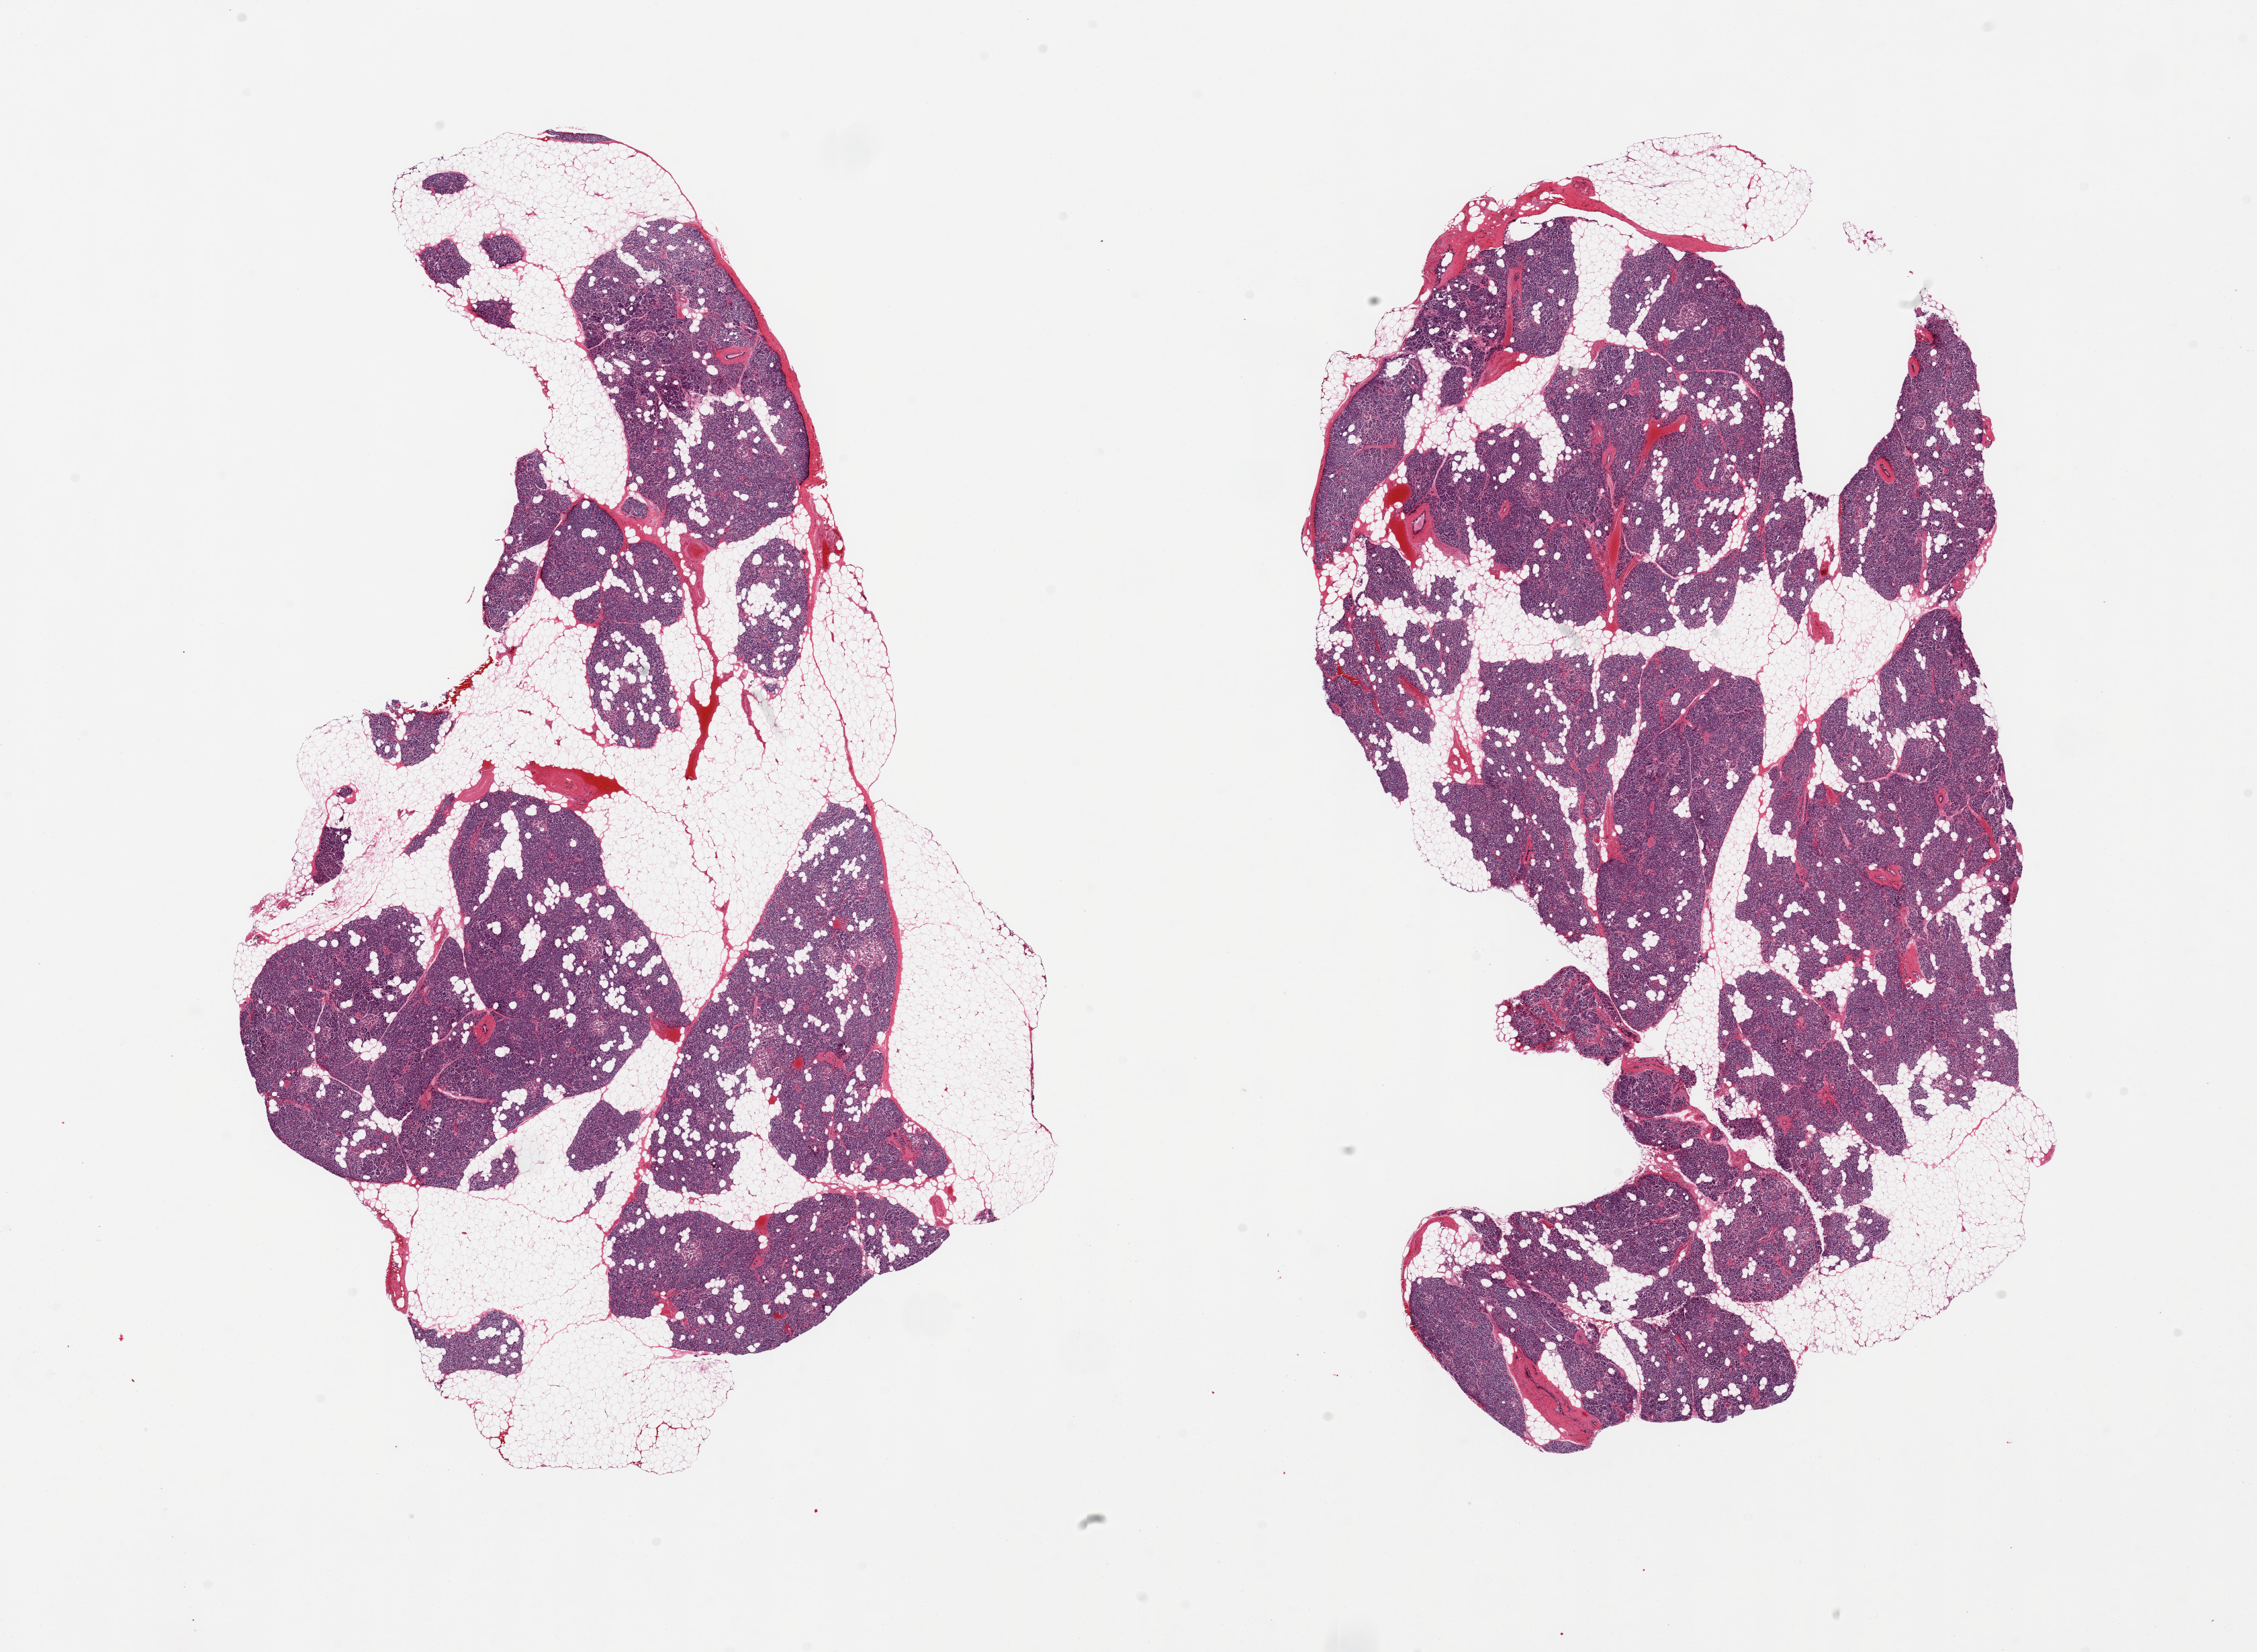
Digitized haematoxylin and eosin-stained section, shown as a low-resolution overview of the whole scanned area (about 26.6 x 19.5 mm), PAXgene-fixed, paraffin-embedded tissue, sampled site (target tissue): pancreas, donor tissue sample. Donor: female.
Review note (as recorded): 2 pieces, up to 50% interstital fat; Islets well visualized; Some areas approach score 2/saponification/autolysis.